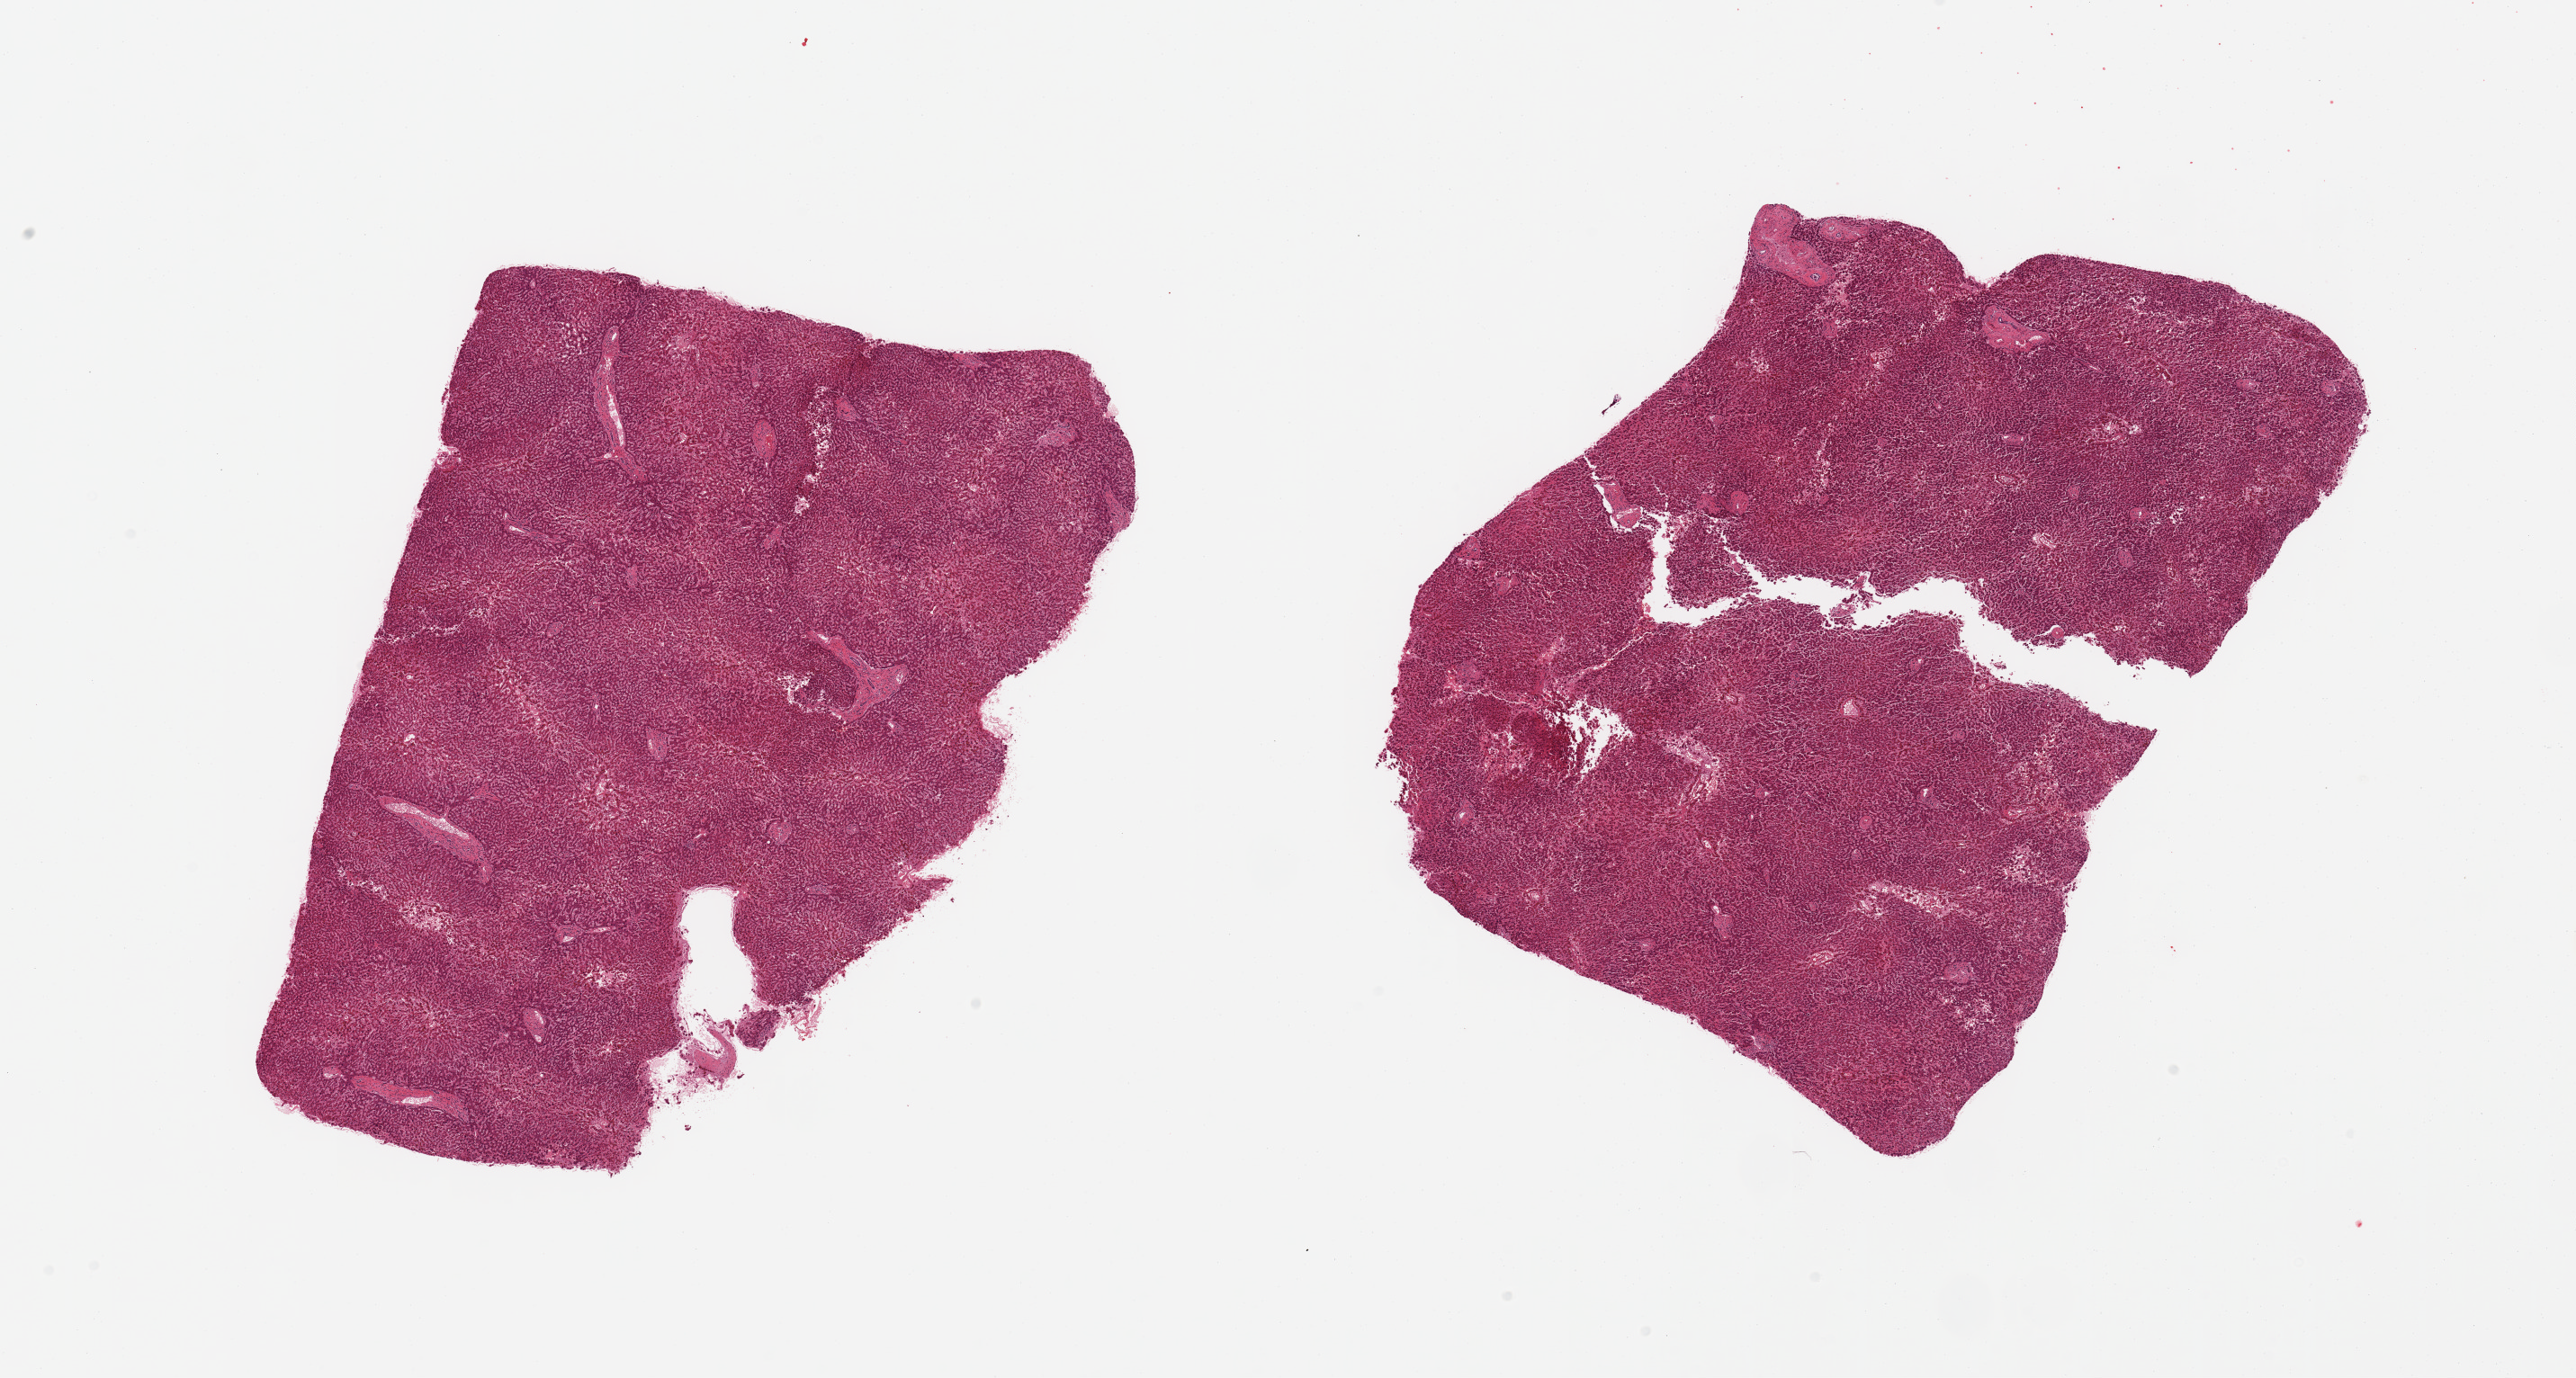
Whole-slide image, haematoxylin and eosin stain — shown as a low-resolution overview of the whole scanned area (about 22.6 x 12.1 mm, acquisition: 20x scan). PAXgene-fixed paraffin-embedded (PFPE) section. Section of liver (target tissue). Tissue donor sample. Donor sex: female.
* pathologist's review note for this sample: 2 pieces, moderate passive congestion